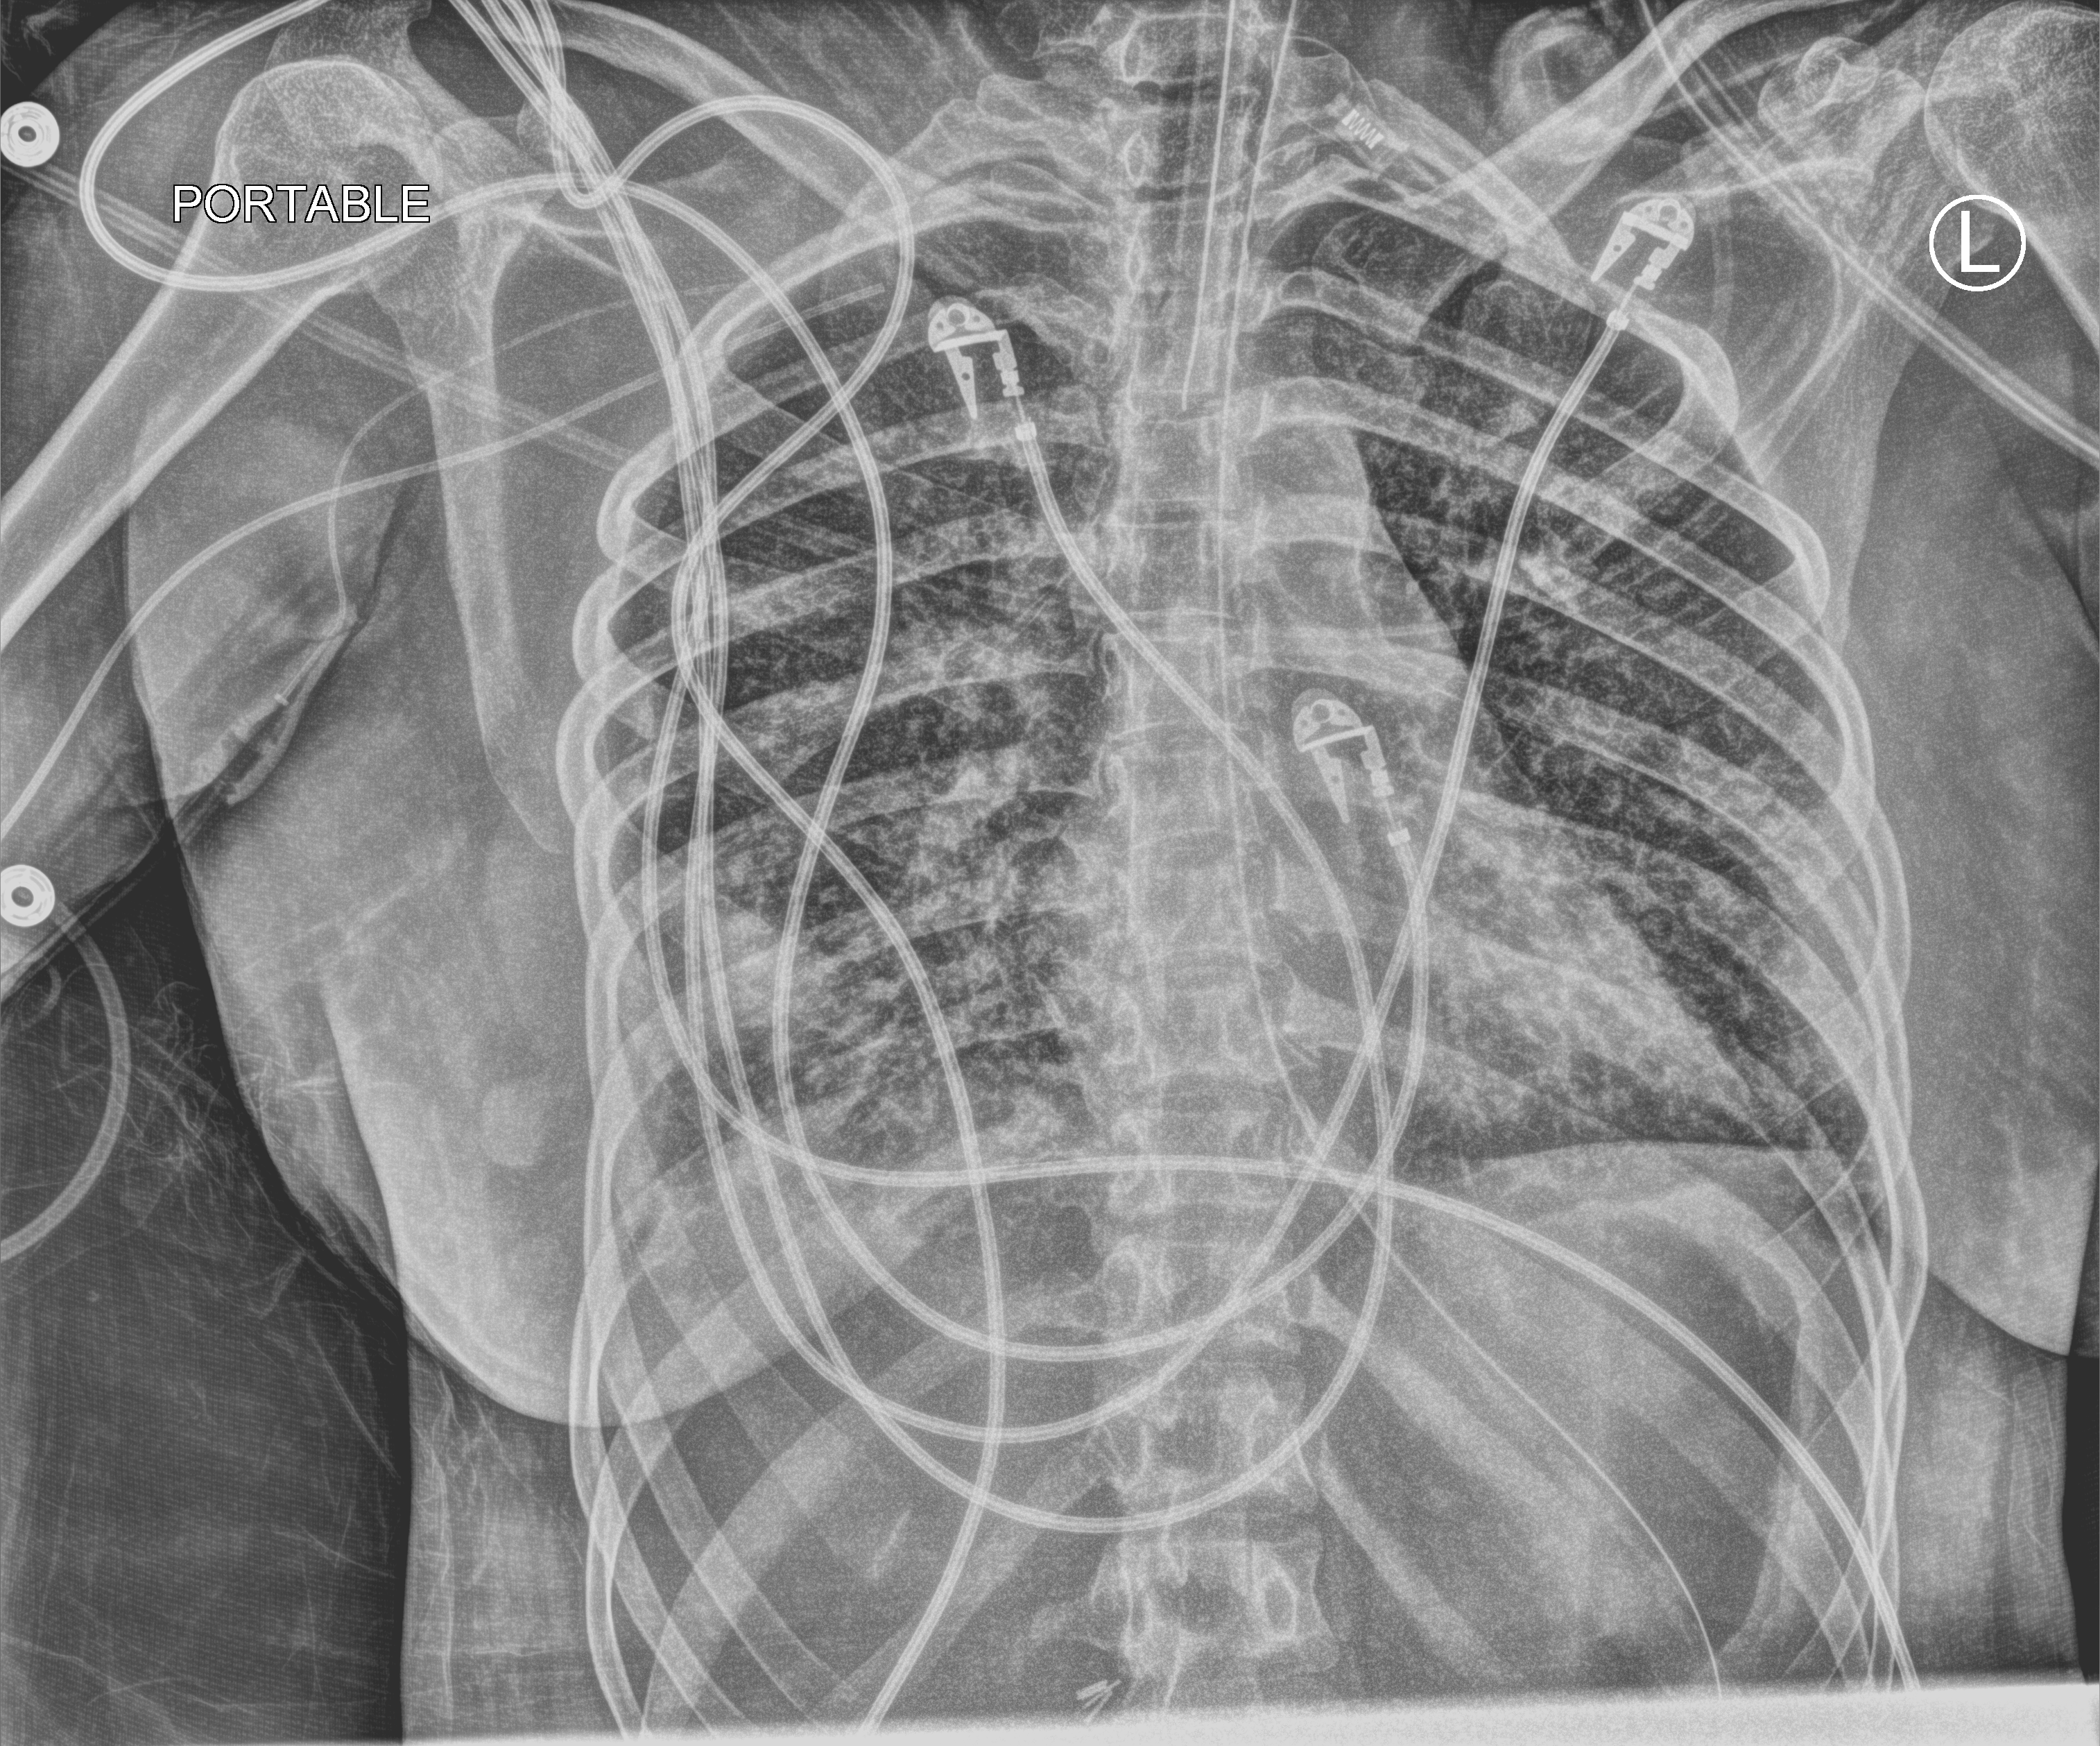
Chest X-ray (portable); anteroposterior (AP) projection. Patient hospitalised with COVID-19, aged 18–59 years.
Admission-level facts for this patient (not findings on this image; timing relative to this image not recorded):
- mechanically ventilated during this hospital stay: yes